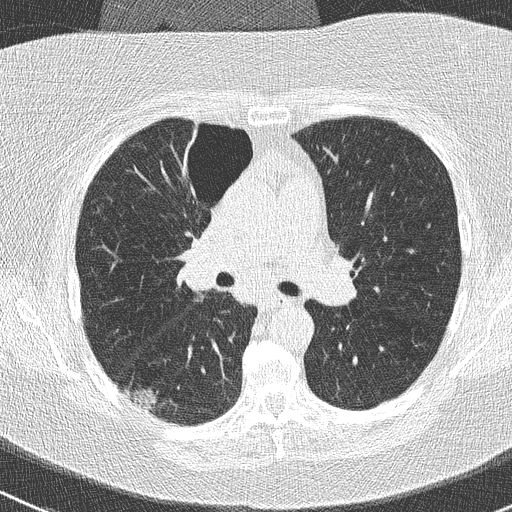
Low-dose screening chest CT, one axial slice. Position 160 of 261 along the scan axis. Reconstruction kernel B50f. Lung window (W 1500 / L -600 HU). 2 mm slice thickness. 512 × 512 image matrix, field of view 310 × 310 mm.
Annotated regions visible in this slice (expert manual segmentation):
- lesion 1 (tumor, lower lobe of right lung): bounding box <133,389,157,410> (left, top, right, bottom; pixels)